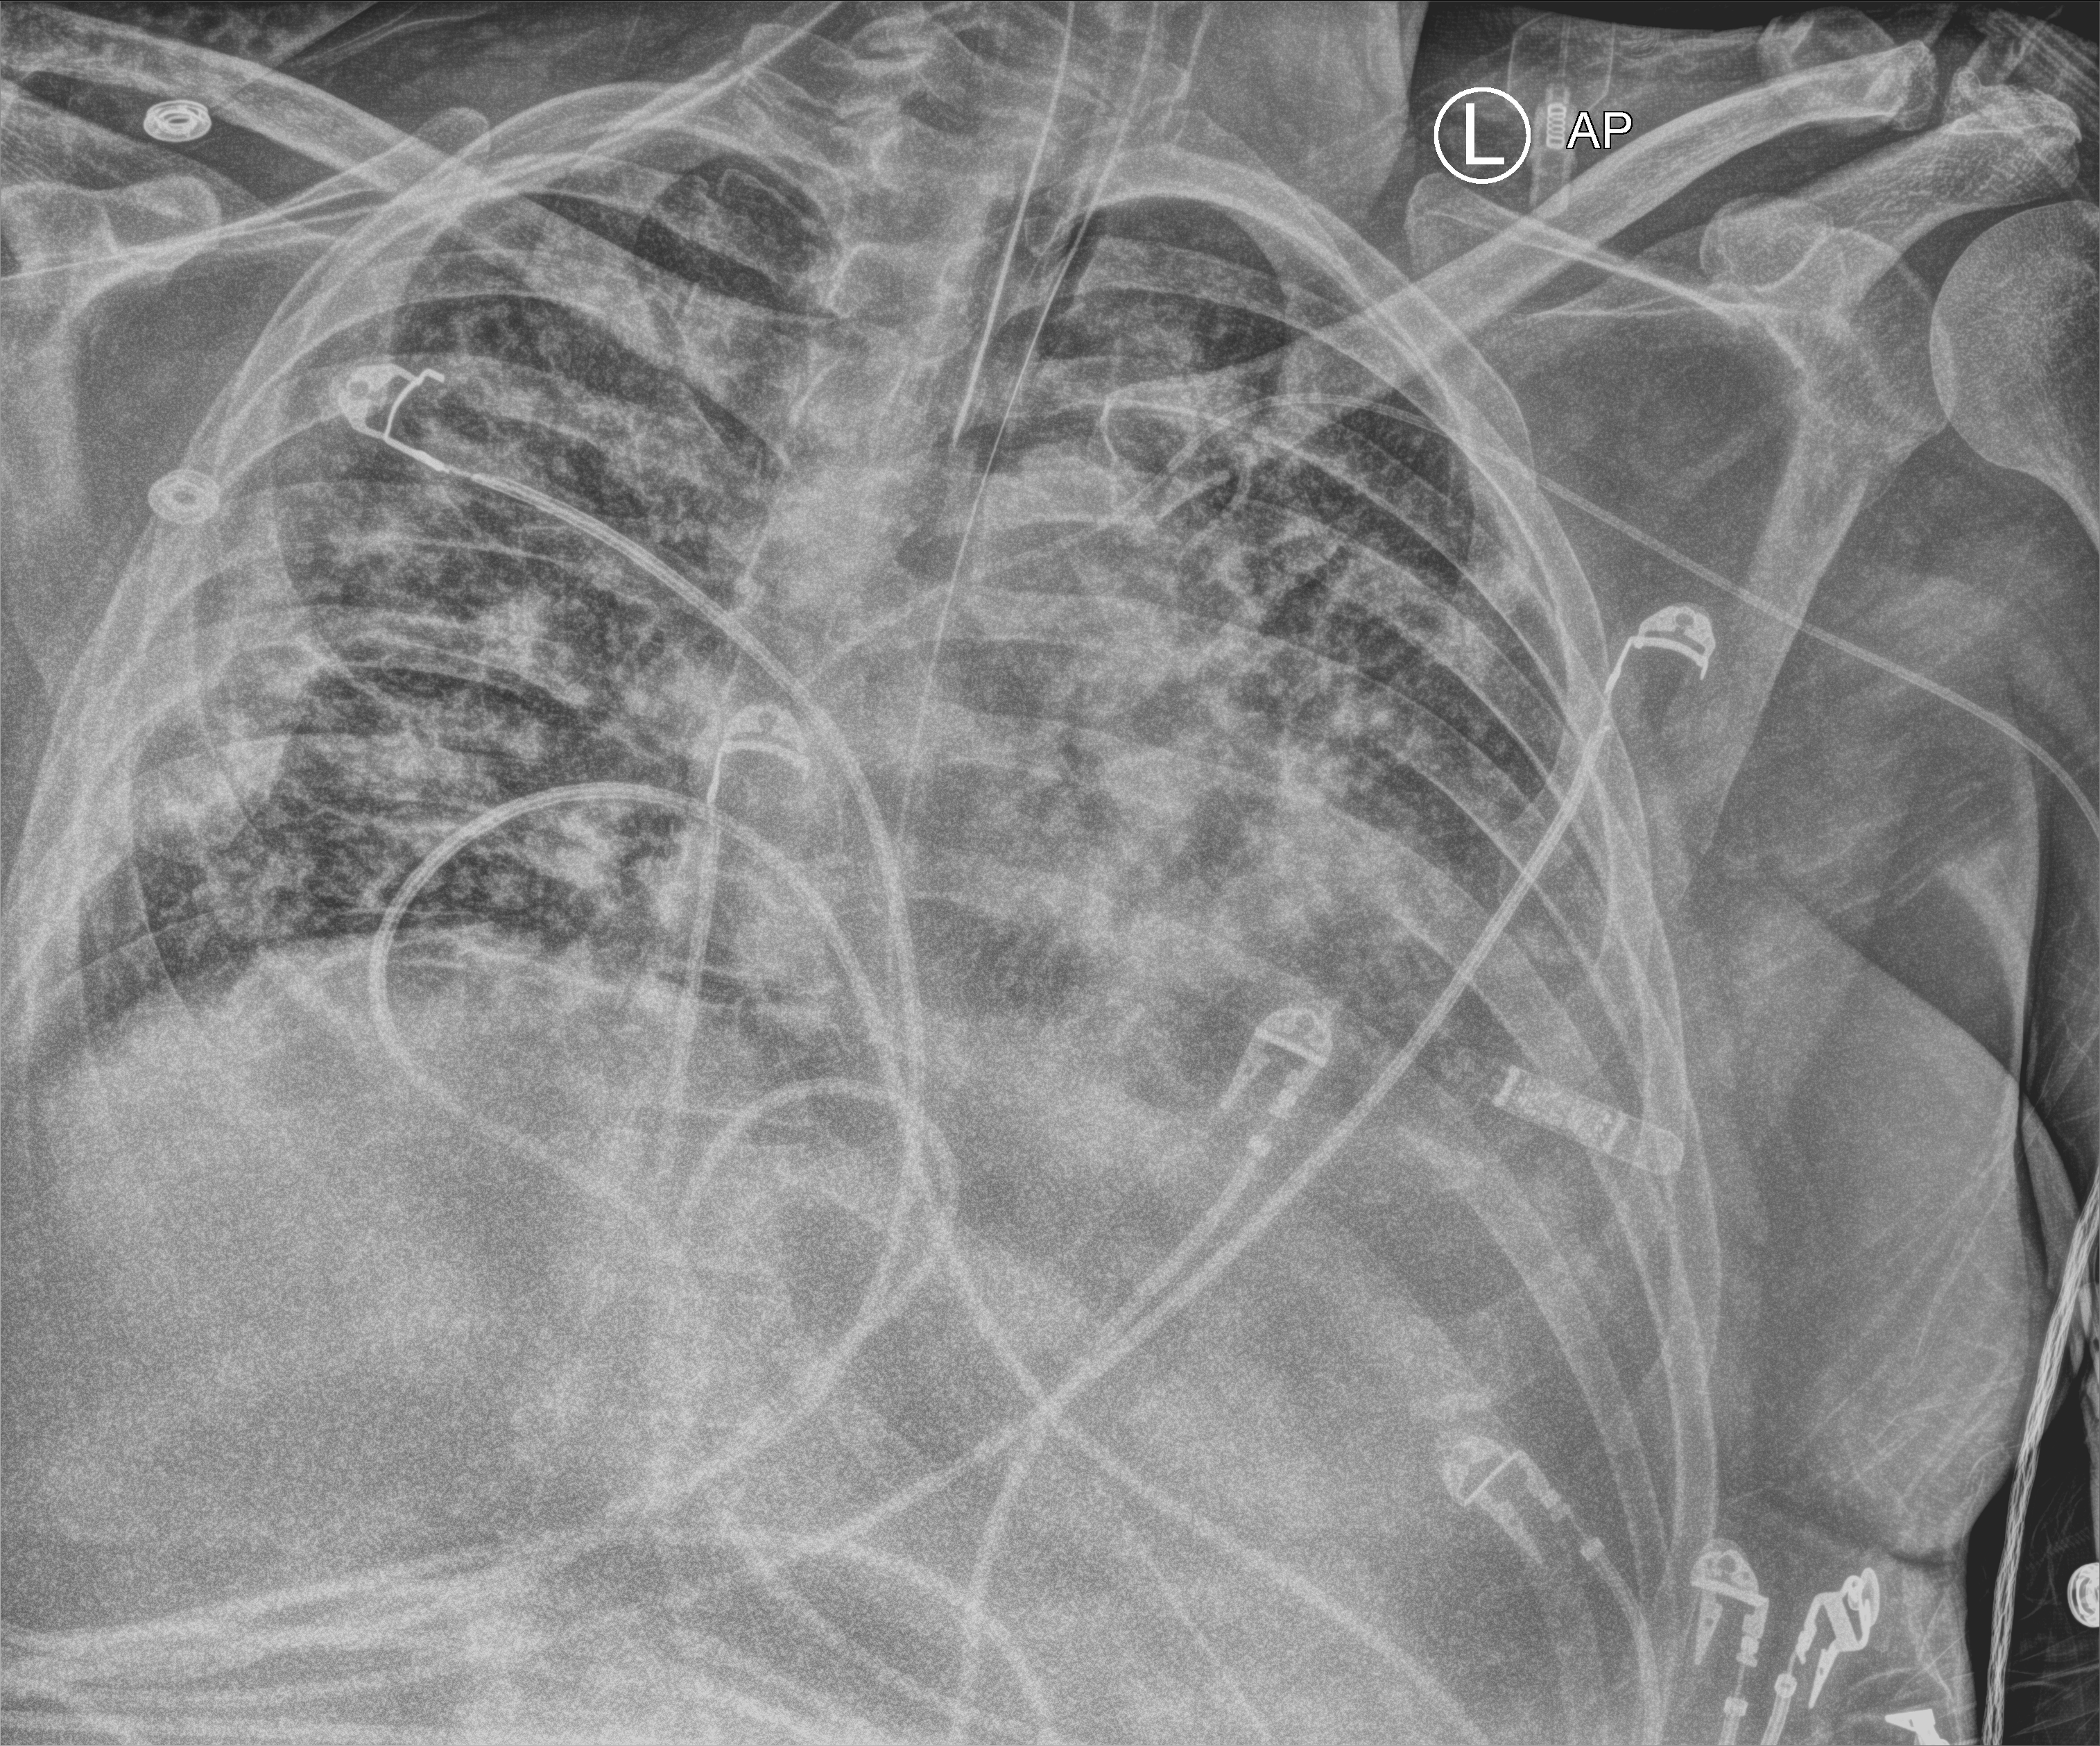
Chest X-ray (portable), anteroposterior (AP) projection. Patient hospitalised with COVID-19; male, aged 18–59 years.
Hospital-stay facts (about this admission, not read from this image; timing relative to this image not recorded): diabetes (admission record): no.